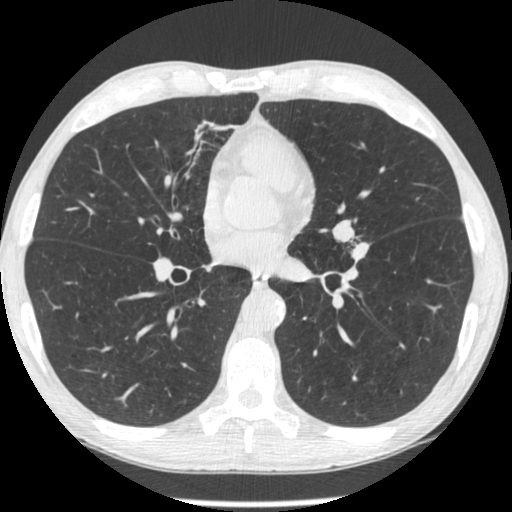
Low-dose screening chest CT, one axial slice; slice 132 of 293 in the series (ordered by position); 120 kVp; lung window (W 1500 / L -600 HU); 1.25 mm slice thickness; 512 × 512 image matrix, field of view 326 × 326 mm.
Structures marked on this image (outlined manually by an expert reader):
- lesion 1 (tumor, upper lobe of left lung): bounding box [x1, y1, x2, y2] px = [352, 242, 369, 260]